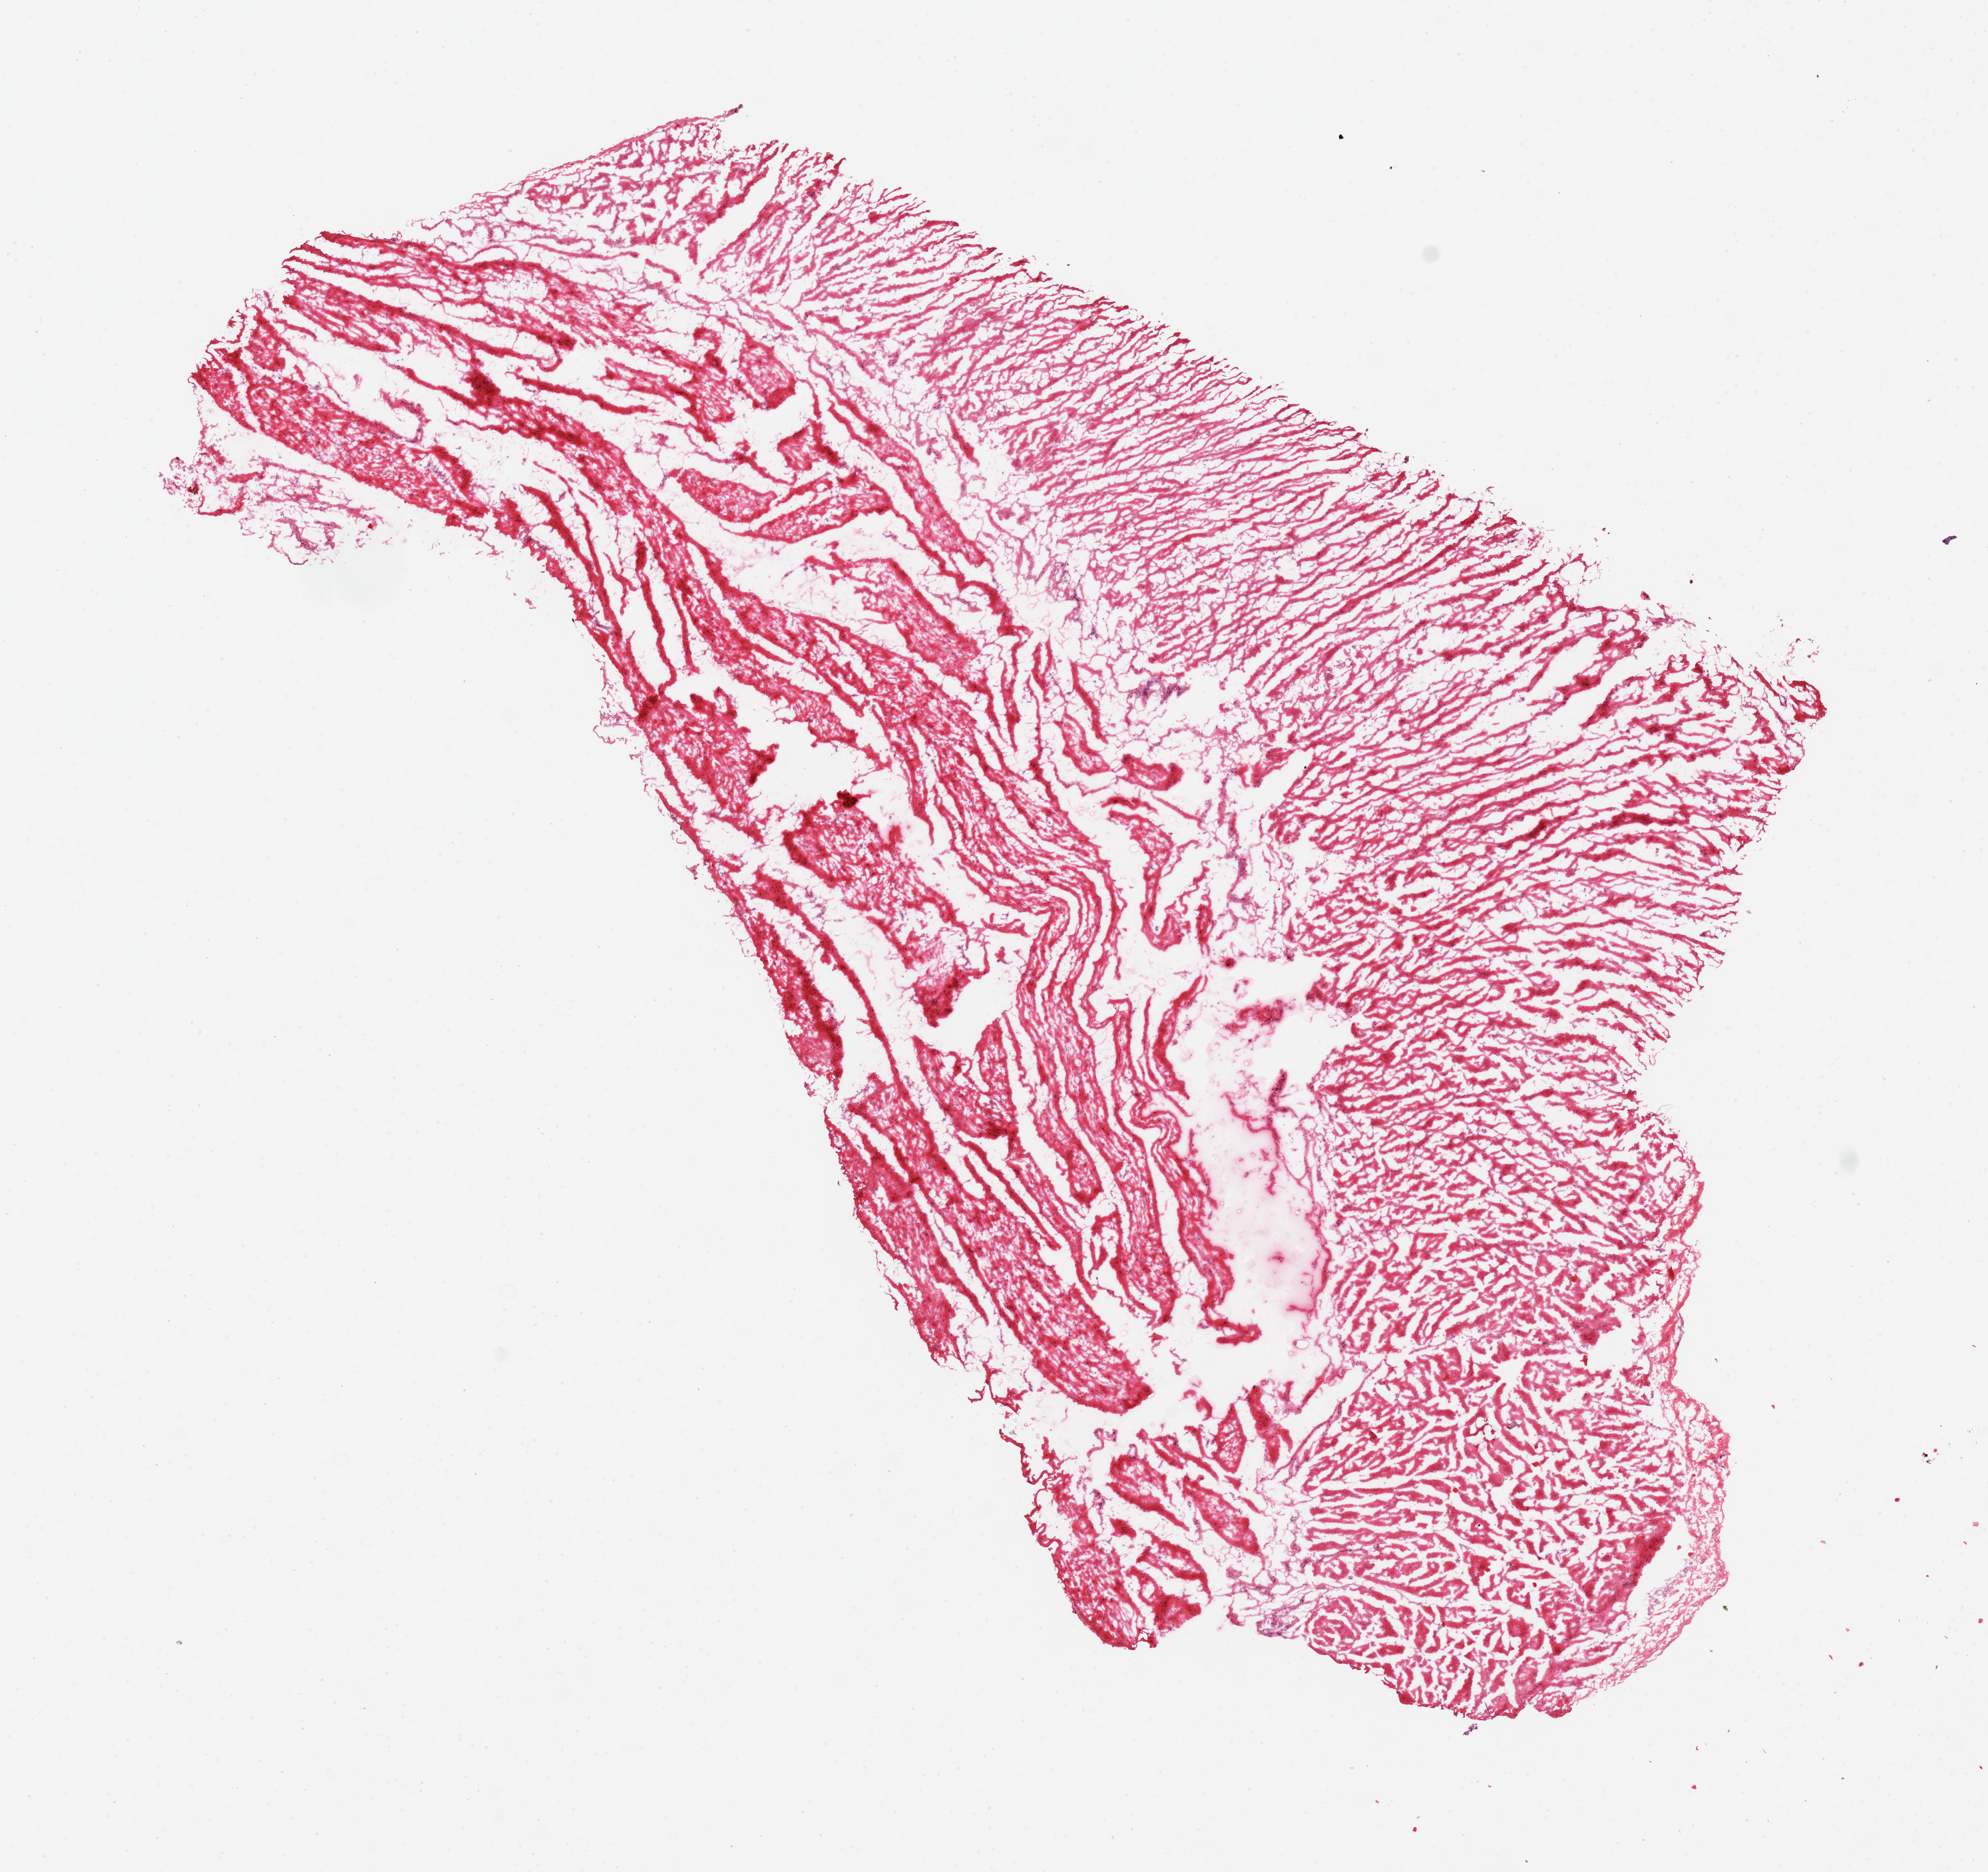
Digitized H&E-stained section, whole scanned area (about 11.8 x 11.1 mm) shown as a low-resolution overview. Frozen section (dry ice). Sampled site (target tissue): esophageal muscle. Donor tissue sample. Donor: female.
Review note (as recorded): 1 piece.